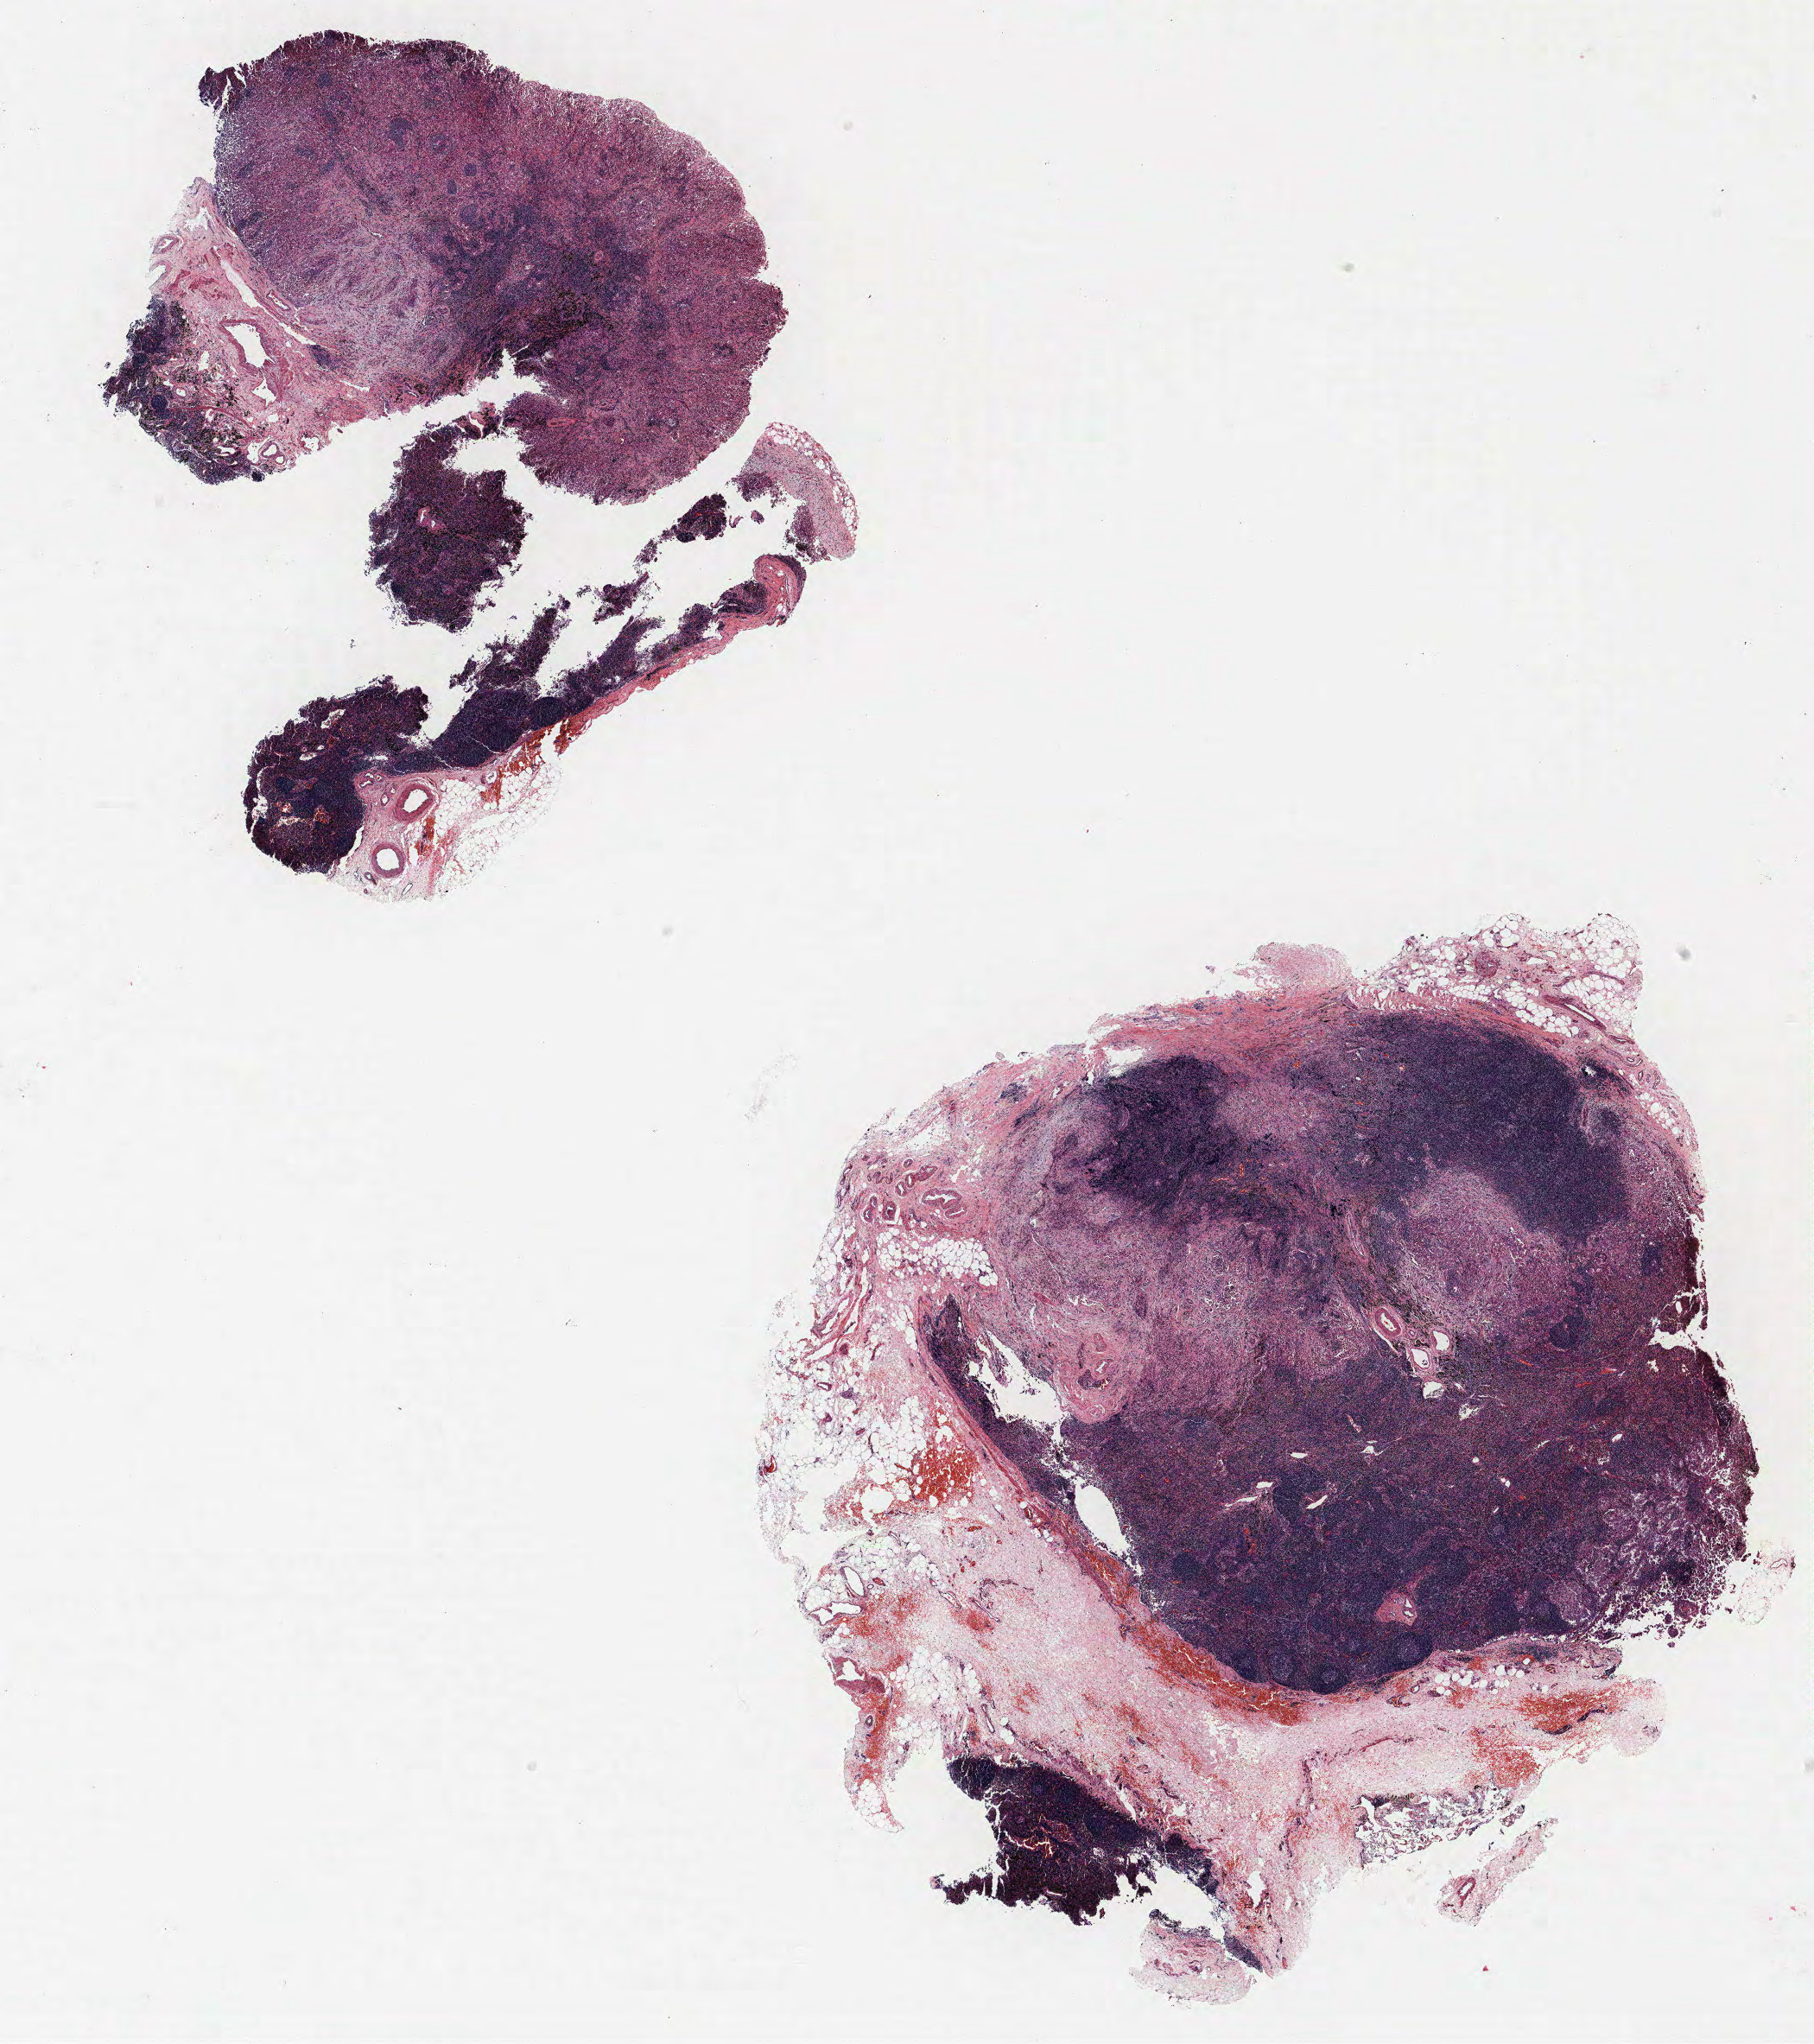
Hematoxylin and eosin (H&E) stained whole-slide image, whole scanned area (about 16.8 x 18.9 mm, acquisition: 40x scan) shown as a low-resolution overview. FFPE section. Lung tissue. Male, age 71 at enrolment. Grade: moderately differentiated (G2).
- primary tumour location (clinical record): left upper lobe
- tumour size (pathology): 35 mm
- stage (AJCC 6th edition): IIB
- participant's lung-cancer diagnosis: Bronchiolo-alveolar adenocarcinoma, NOS